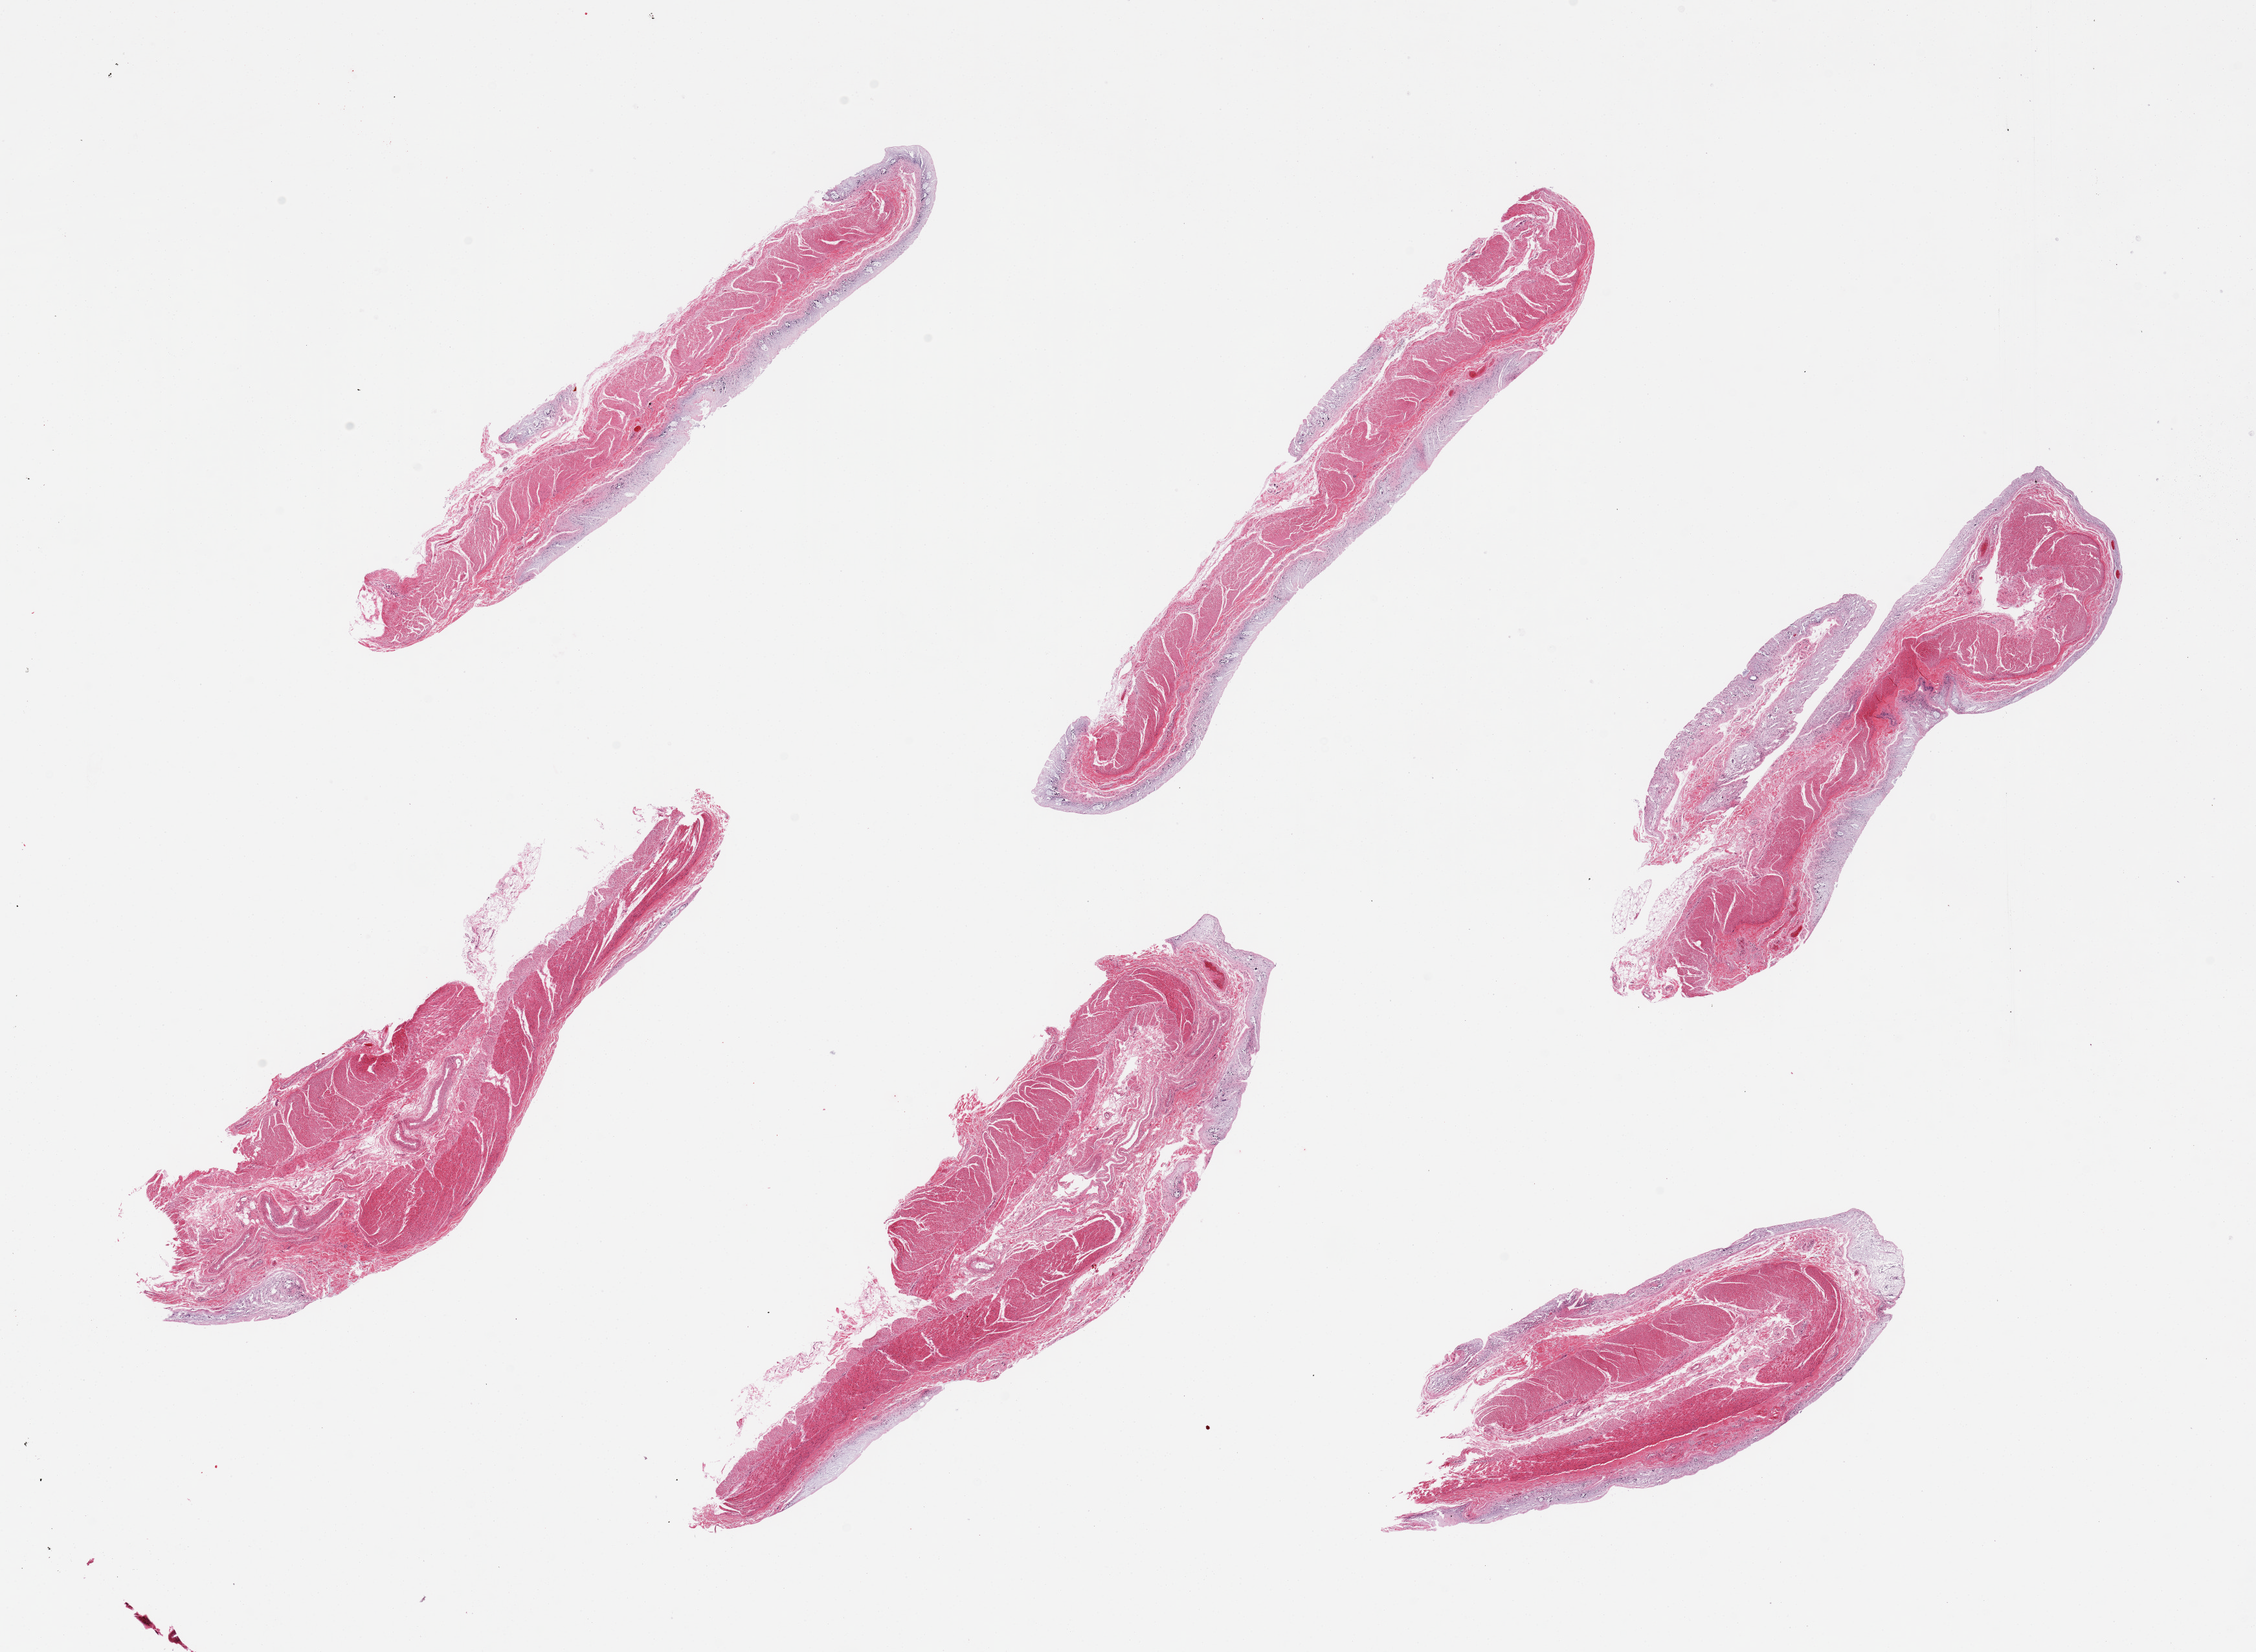
H&E whole-slide image, whole scanned area (about 27.6 x 20.2 mm, slide scanned at 20x) shown as a low-resolution overview.
- specimen: PAXgene-fixed paraffin-embedded (PFPE) section; sampled site (target tissue): transverse colon; donor tissue sample